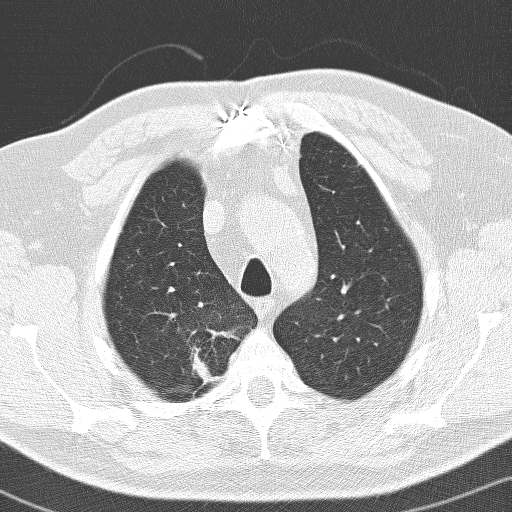
Low-dose screening chest CT, one axial slice. Slice 117 of 141 in the series (ordered by position). Lung window (W 1500 / L -600 HU). 3.2 mm slice thickness. 512 × 512 image matrix, field of view 326 × 326 mm.
Outlined on this slice (outlined manually by an expert reader):
- lesion 1 (tumor, upper lobe of right lung): bounding box <193,347,211,381> (left, top, right, bottom; pixels)